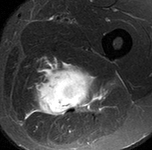
MRI of an extremity soft-tissue mass, one axial slice. Position 81 of 90 along the scan axis. STIR. MR volume resampled by the dataset authors to the PET/CT grid (not the native acquisition matrix). 3.27 mm slice thickness. 152 × 150 image matrix, field of view 148 × 146 mm. Male patient. Case-level facts recorded for this patient, not image findings: histological type: undifferentiated pleomorphic liposarcoma; grade: high; site of the primary tumour: left thigh.
Annotated regions visible in this slice (expert contour drawn on MRI and transferred to this co-registered scan by the dataset authors):
- gross tumour volume including surrounding oedema: bounding box [x1, y1, x2, y2] px = [29, 62, 108, 120]
- gross tumour volume (mass): [34, 64, 99, 118]